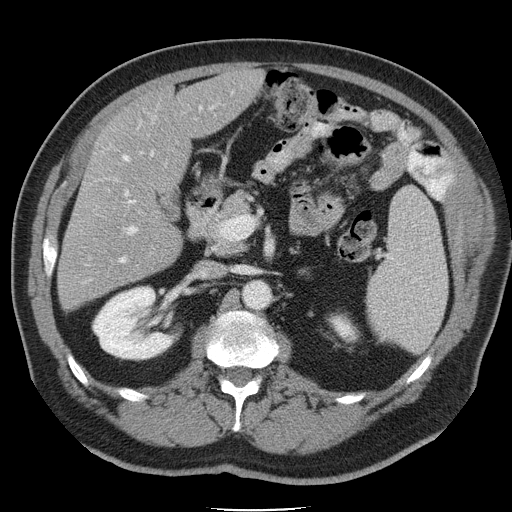
Contrast-enhanced abdominal CT, one axial slice. Position 21 of 45 along the scan axis. 120 kVp. Intravenous contrast given. Soft-tissue window (W 400 / L 40 HU). 5 mm slice thickness. 512 × 512 image matrix. Male patient, age 65 years. From the clinical record (not read from this slice): diagnosis: colorectal cancer liver metastases, imaged before liver resection; multiple liver metastases: yes; largest metastasis: 4.9 cm; disease in both lobes: no.
Outlined on this slice (outlined manually by an expert reader):
- hepatic veins: box from (x=118, y=107) to (x=213, y=263) px
- liver: (x=58, y=68)–(x=264, y=309)
- planned liver remnant (the part of the liver to remain after resection): (x=97, y=68)–(x=264, y=187)
- portal vein (with intrahepatic branches): (x=125, y=191)–(x=137, y=234)